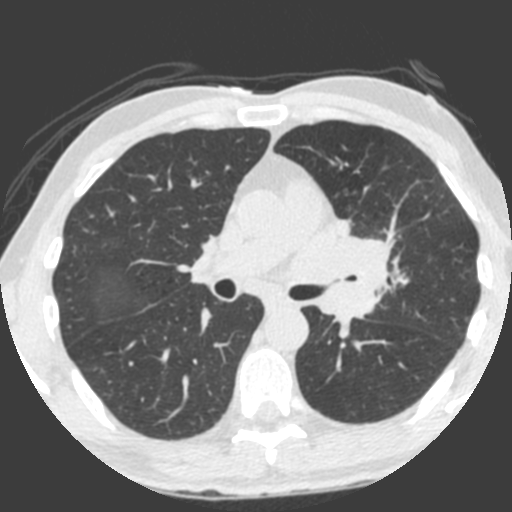
Low-dose screening chest CT, one axial slice; position 131 of 212 along the scan axis; 120 kVp; lung window (W 1500 / L -600 HU); 512 × 512 image matrix.
Structures marked on this image (expert manual segmentation):
- lesion 1 (tumor, upper lobe of left lung): box from (x=316, y=219) to (x=389, y=324) px